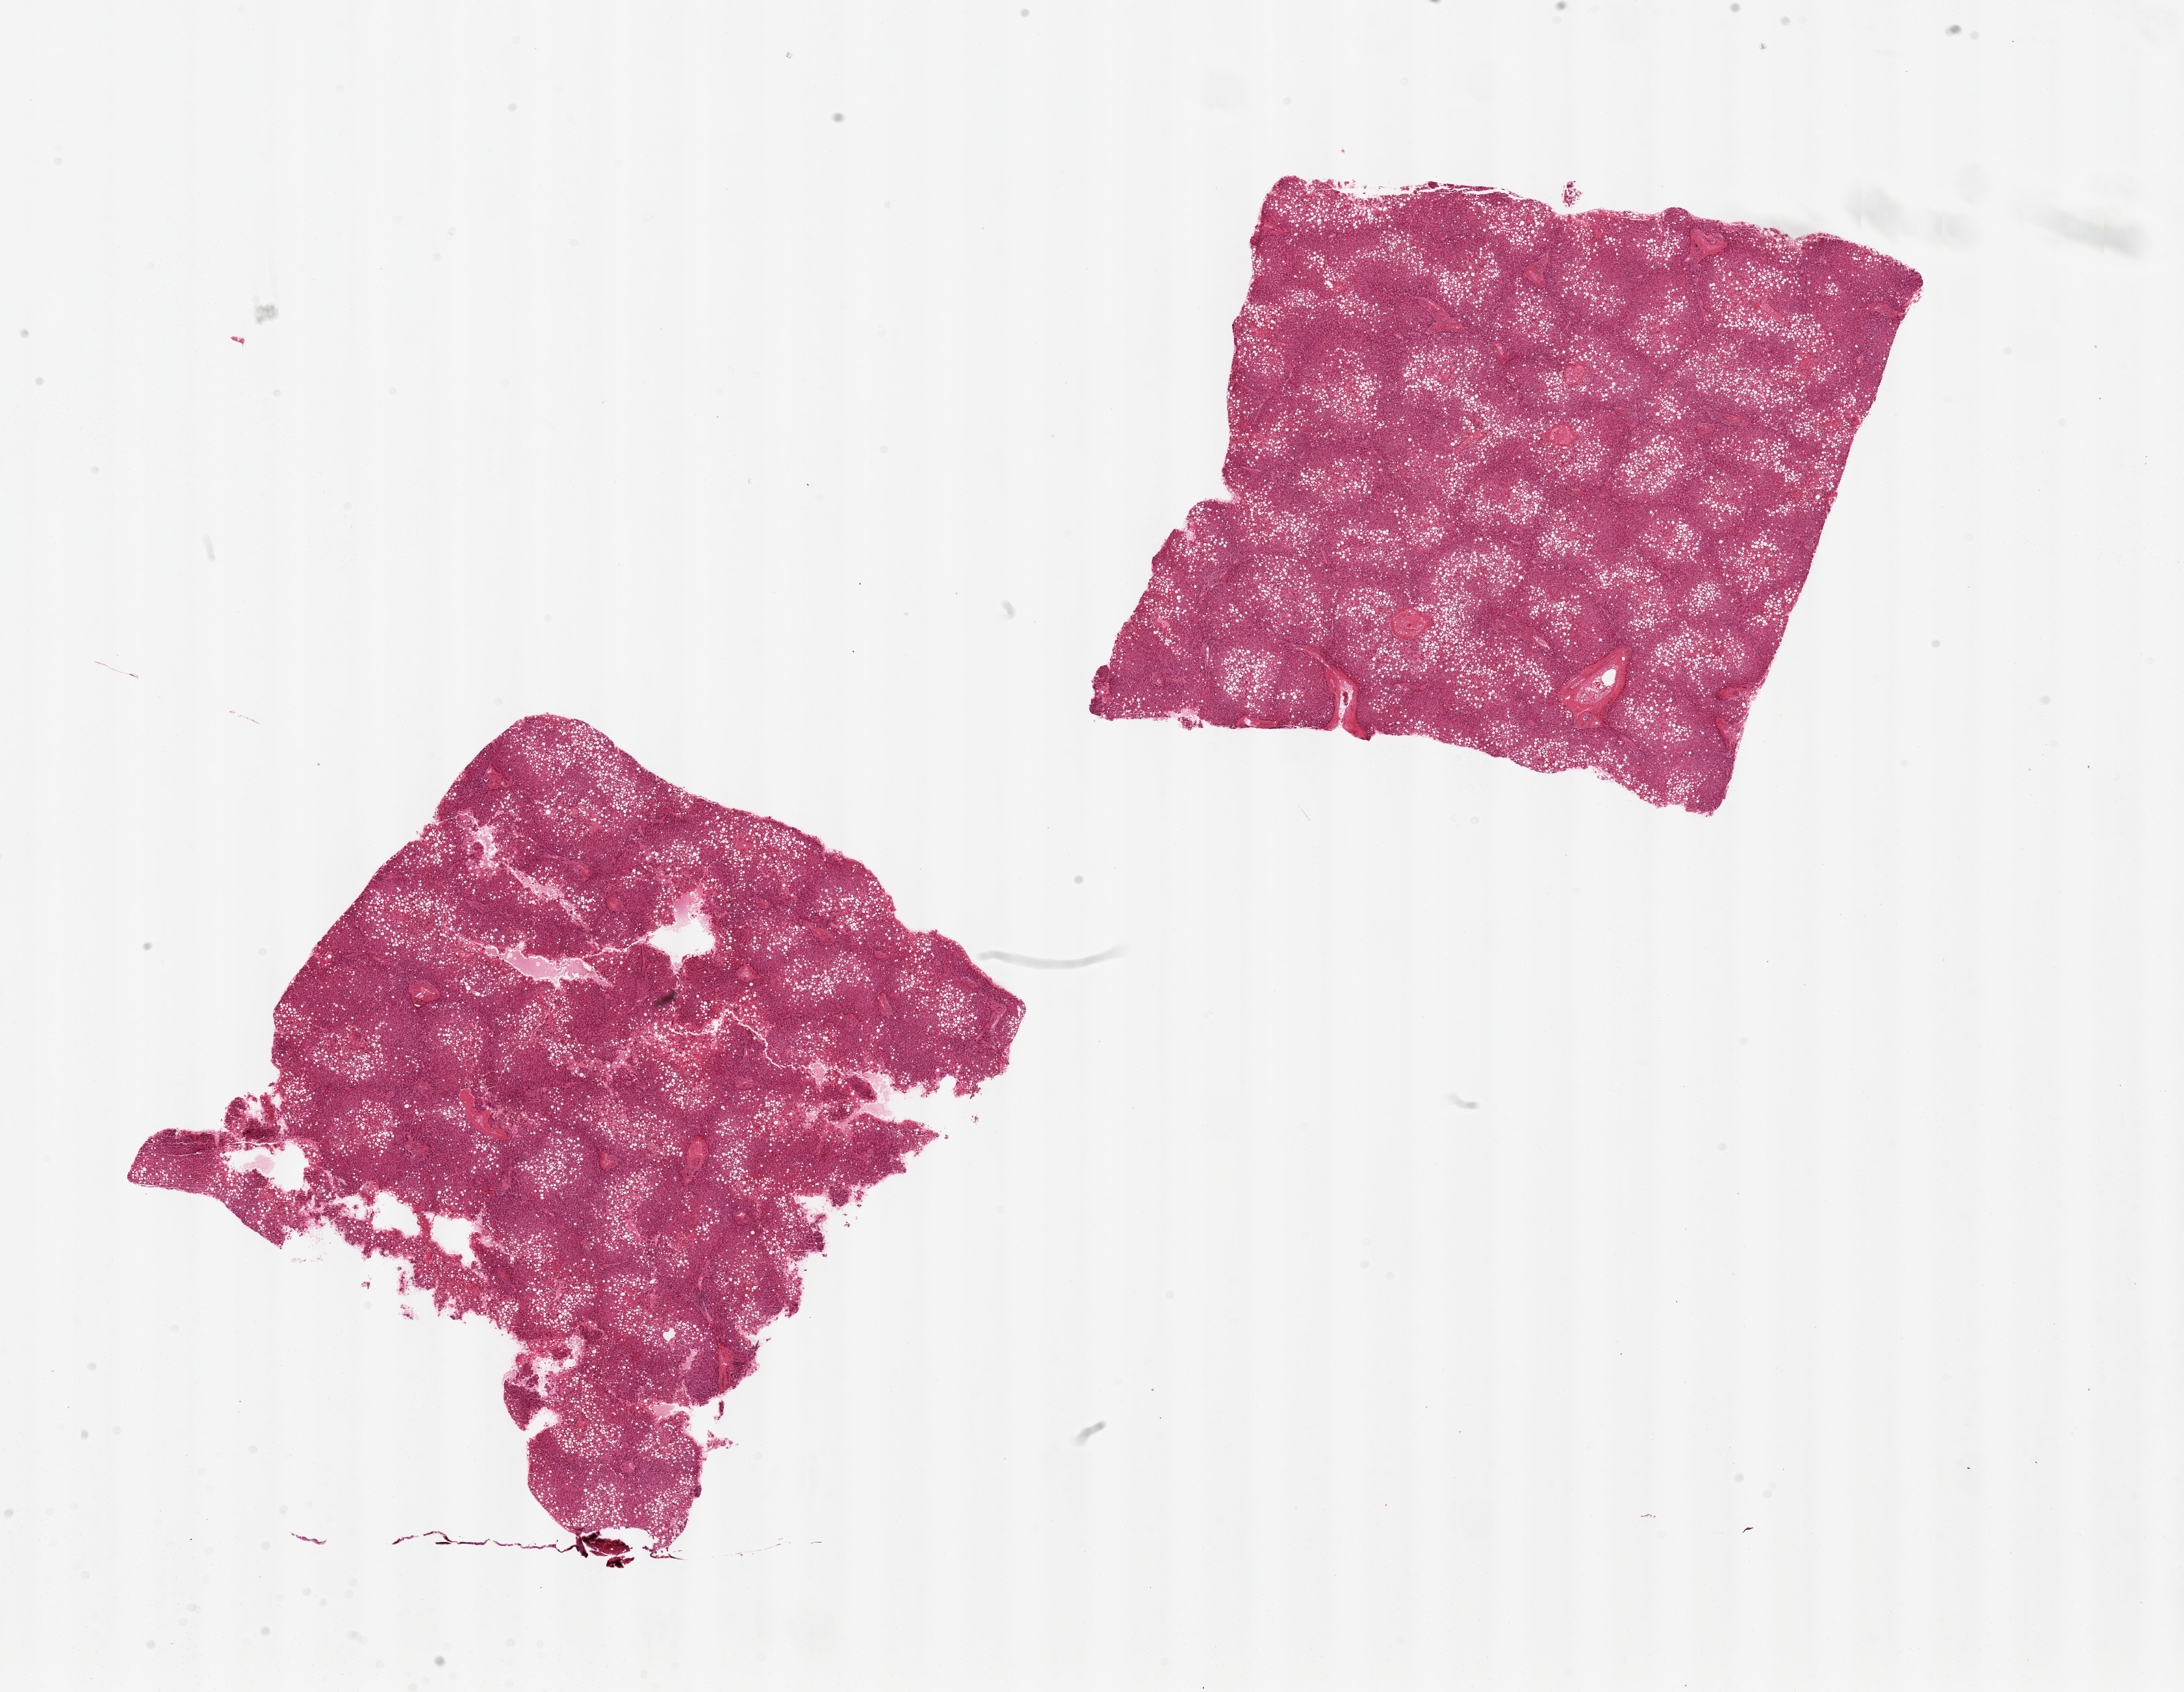
Digitized hematoxylin and eosin (H&E)-stained section, brightfield — a low-resolution overview of the entire scanned area, about 26.6 x 20.6 mm, PAXgene-fixed paraffin-embedded (PFPE) section, sampled site (target tissue): liver, donor tissue sample. Donor: male.
* reviewer comment on this tissue sample: 2 pieces, moderate steatosis, passive congestion